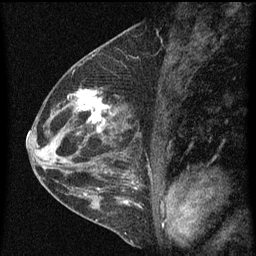
Breast MRI (dynamic contrast-enhanced), one sagittal slice; position 28 of 60 along the scan axis; dynamic contrast-enhanced series, image 2 of 4 at this slice position (ordered by acquisition); 1.5 T; TE 4.2 ms, TR 8 ms; 2 mm slice thickness; 256 × 256 image matrix, field of view 180 × 180 mm. Female patient, age 48 years.
Structures marked on this image (semi-automatic segmentation, software-assisted and operator-edited):
- analysis volume of interest (the breast-tissue region the enhancement analysis was run in; not a lesion): bounding box (x1, y1, x2, y2) in pixels: (73, 86, 115, 139)
- tumour enhancement mask (voxels above the 70 % enhancement threshold inside the analysis volume of interest): (76, 90, 115, 133)